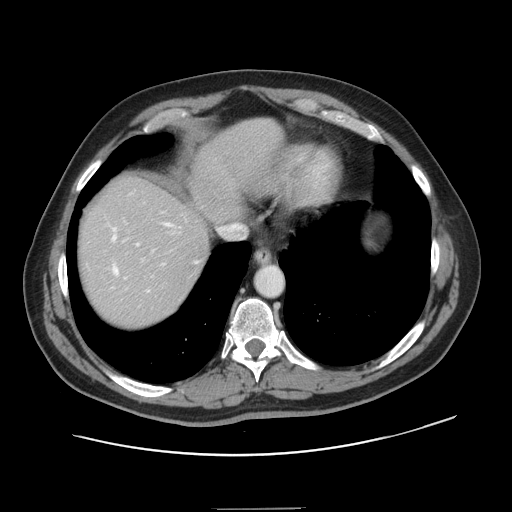
Contrast-enhanced abdominal CT, one axial slice; position 126 of 143 along the scan axis; 120 kVp; intravenous contrast given; soft-tissue window (W 400 / L 40 HU); 512 × 512 image matrix, field of view 402 × 402 mm. Male patient, age 62 years. From the clinical record (not read from this slice): diagnosis: colorectal cancer liver metastases, imaged before liver resection; multiple liver metastases: yes; largest metastasis: 2.7 cm; disease in both lobes: no.
Outlined on this slice (manually delineated by an expert):
- hepatic veins: bounding box [x1, y1, x2, y2] px = [112, 223, 197, 292]
- liver: [78, 118, 283, 328]
- planned liver remnant (the part of the liver to remain after resection): [78, 119, 283, 297]
- portal vein (with intrahepatic branches): [122, 212, 164, 261]